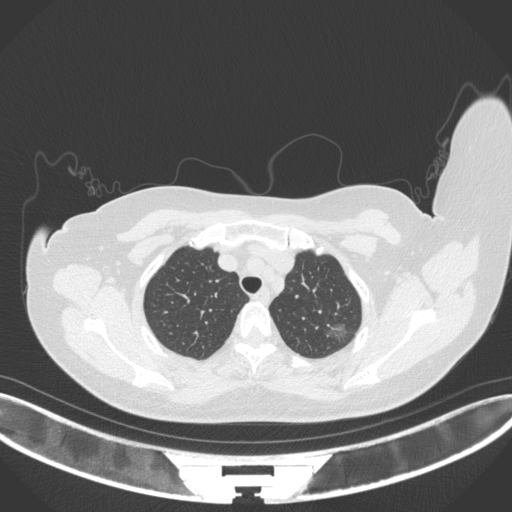
Chest CT, one axial slice; lung window (W 1500 / L -600 HU); 512 × 512 image matrix, field of view 400 × 400 mm. Patient: female, 58 years. Case-level facts recorded for this patient, not image findings: clinical TNM (as recorded): T1c N0 M0.
Outlined on this slice (rectangle marked by the reading radiologist):
- lung tumour (recorded histology: adenocarcinoma): box from (x=324, y=317) to (x=351, y=341) px